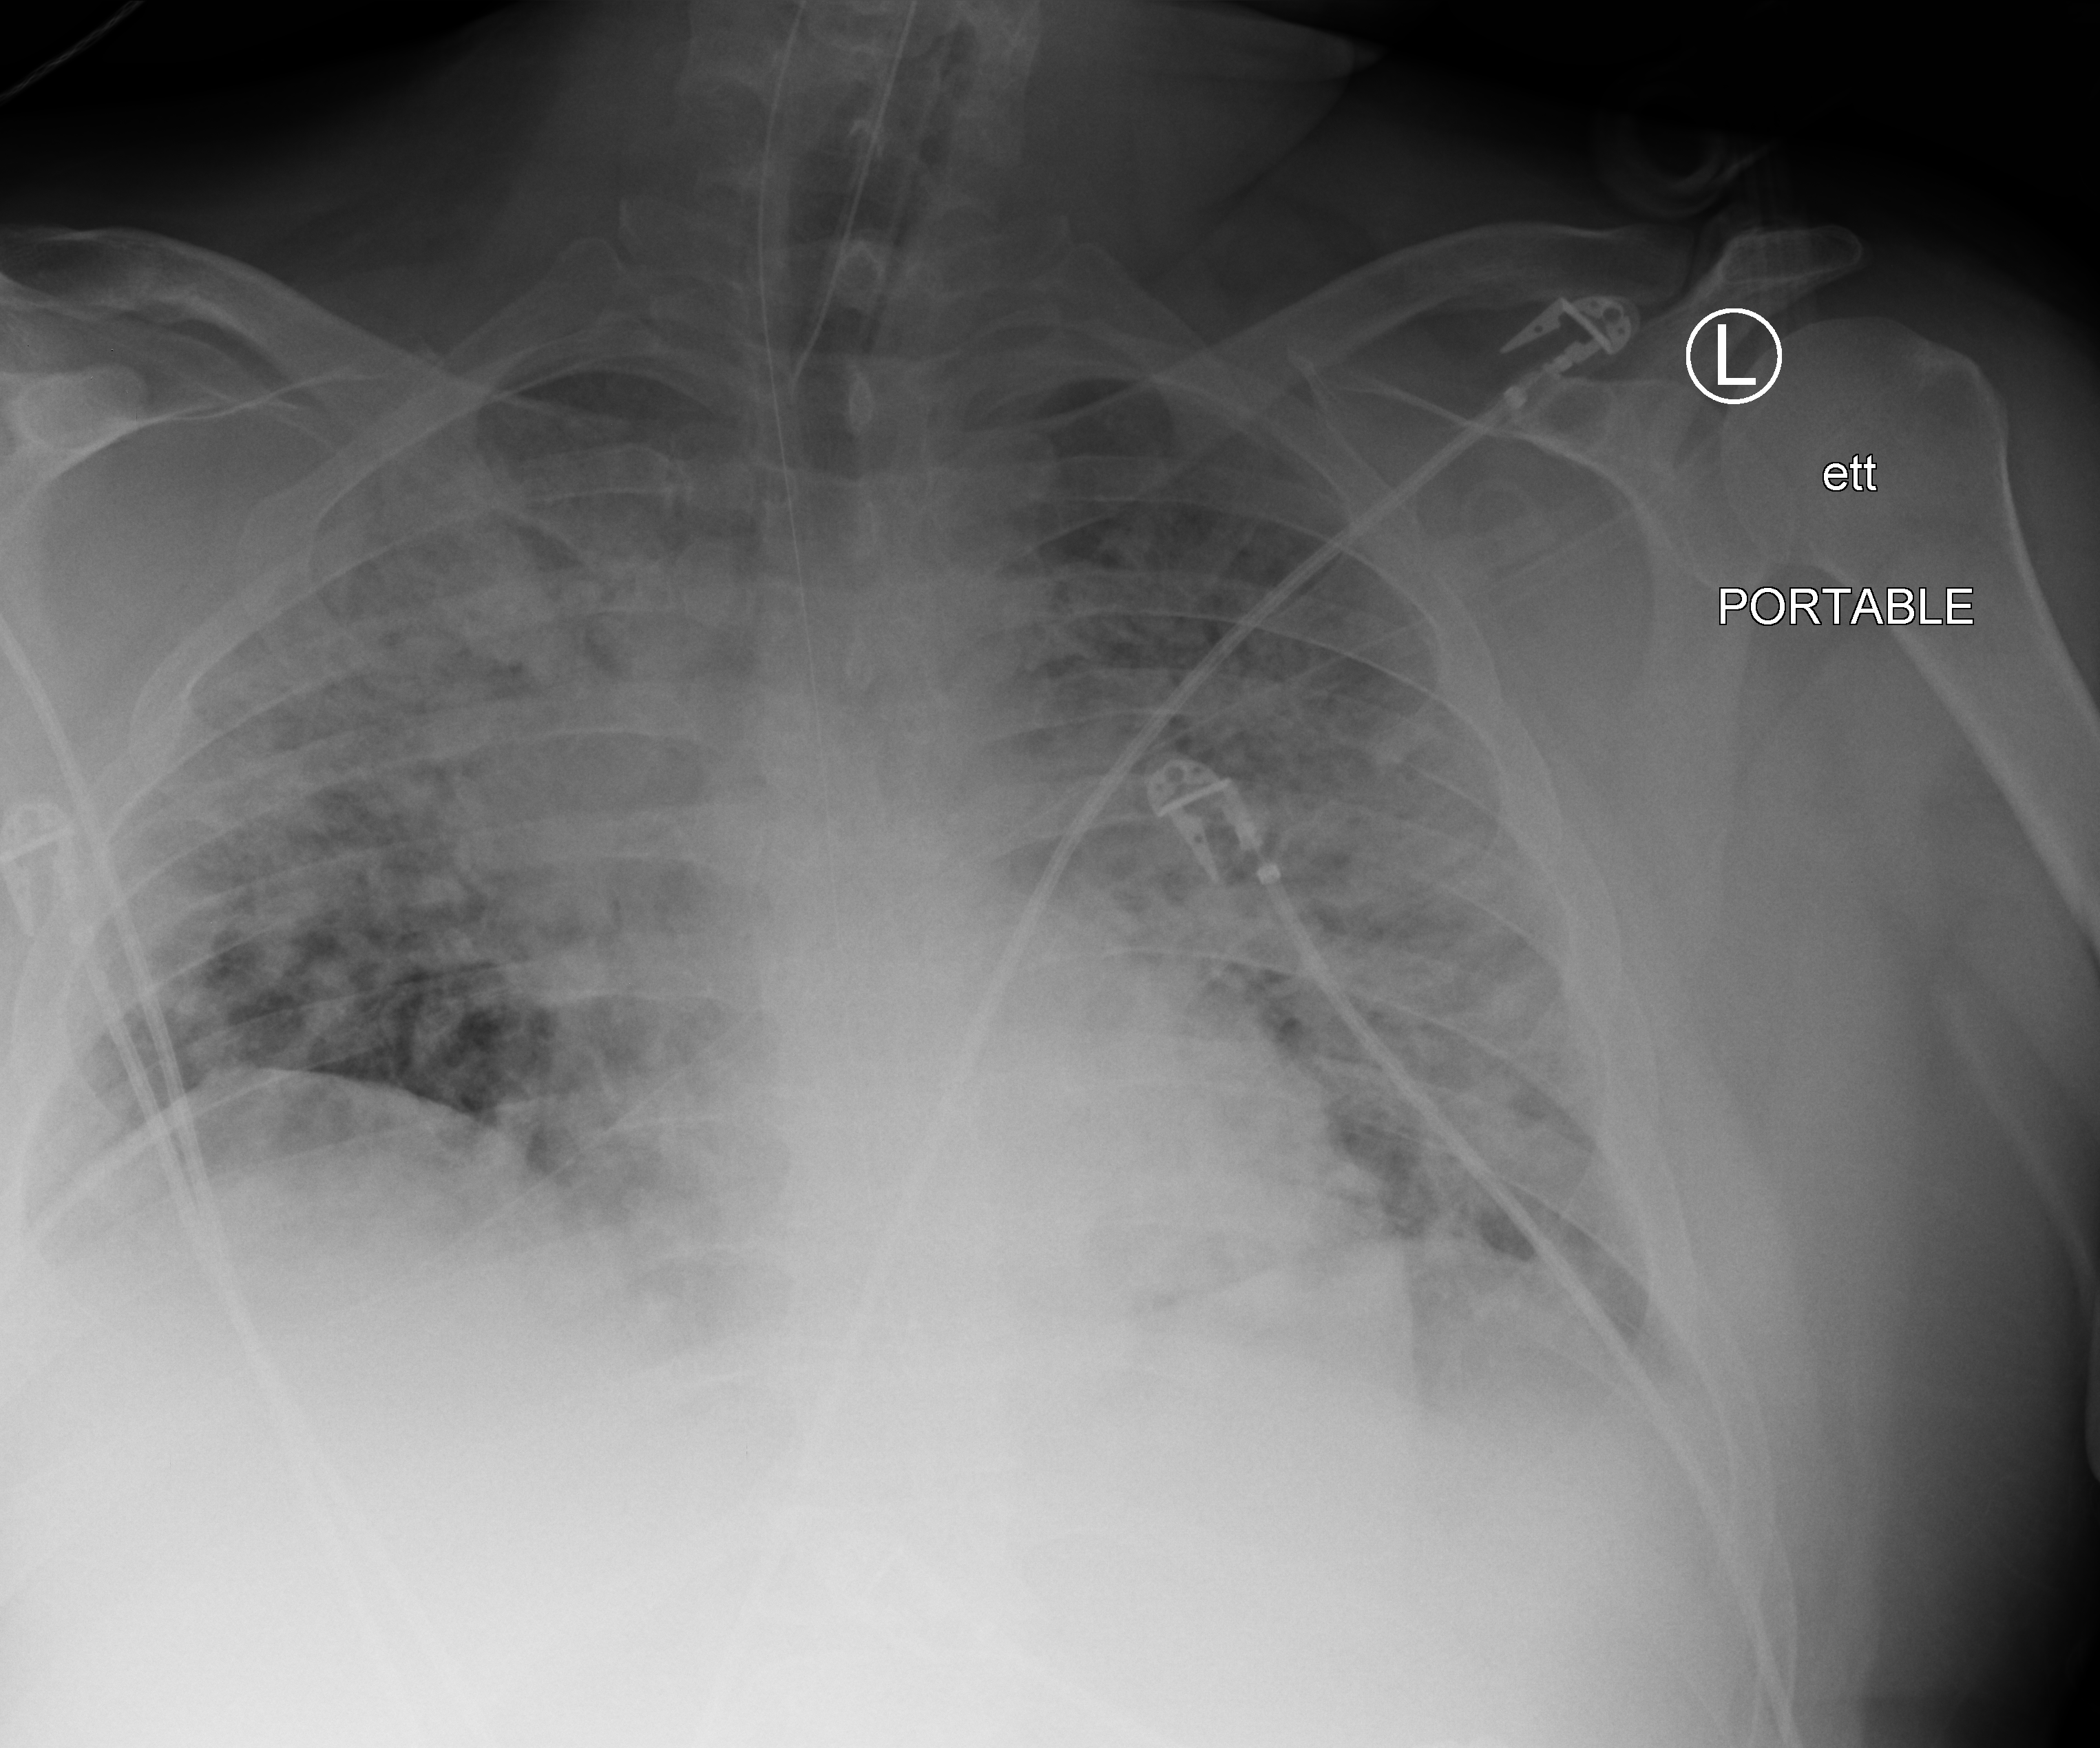
Bedside chest radiograph (computed radiography); anteroposterior (AP) projection. Adult patient hospitalised with COVID-19, age 18–59 years.
From the hospital-stay record, not from the radiograph (when in the stay this image was taken is not recorded):
- admitted to intensive care during this hospital stay: yes
- mechanically ventilated during this hospital stay: yes